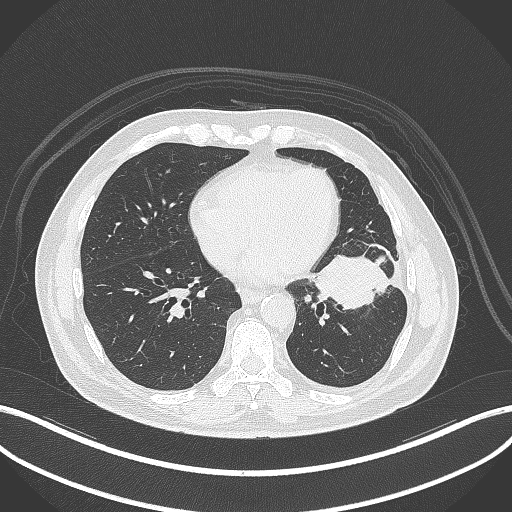
Chest CT, one axial slice. Position 136 of 230 along the scan axis. 120 kVp. Lung window (W 1500 / L -600 HU). 1 mm slice thickness. 512 × 512 image matrix. Male patient, age 68 years. From the clinical record (not read from this slice): clinical TNM (as recorded): T2b N0 M0.
Outlined on this slice (bounding box drawn by a radiologist):
- lung tumour (recorded histology: squamous cell carcinoma): box from (x=312, y=248) to (x=392, y=318) px